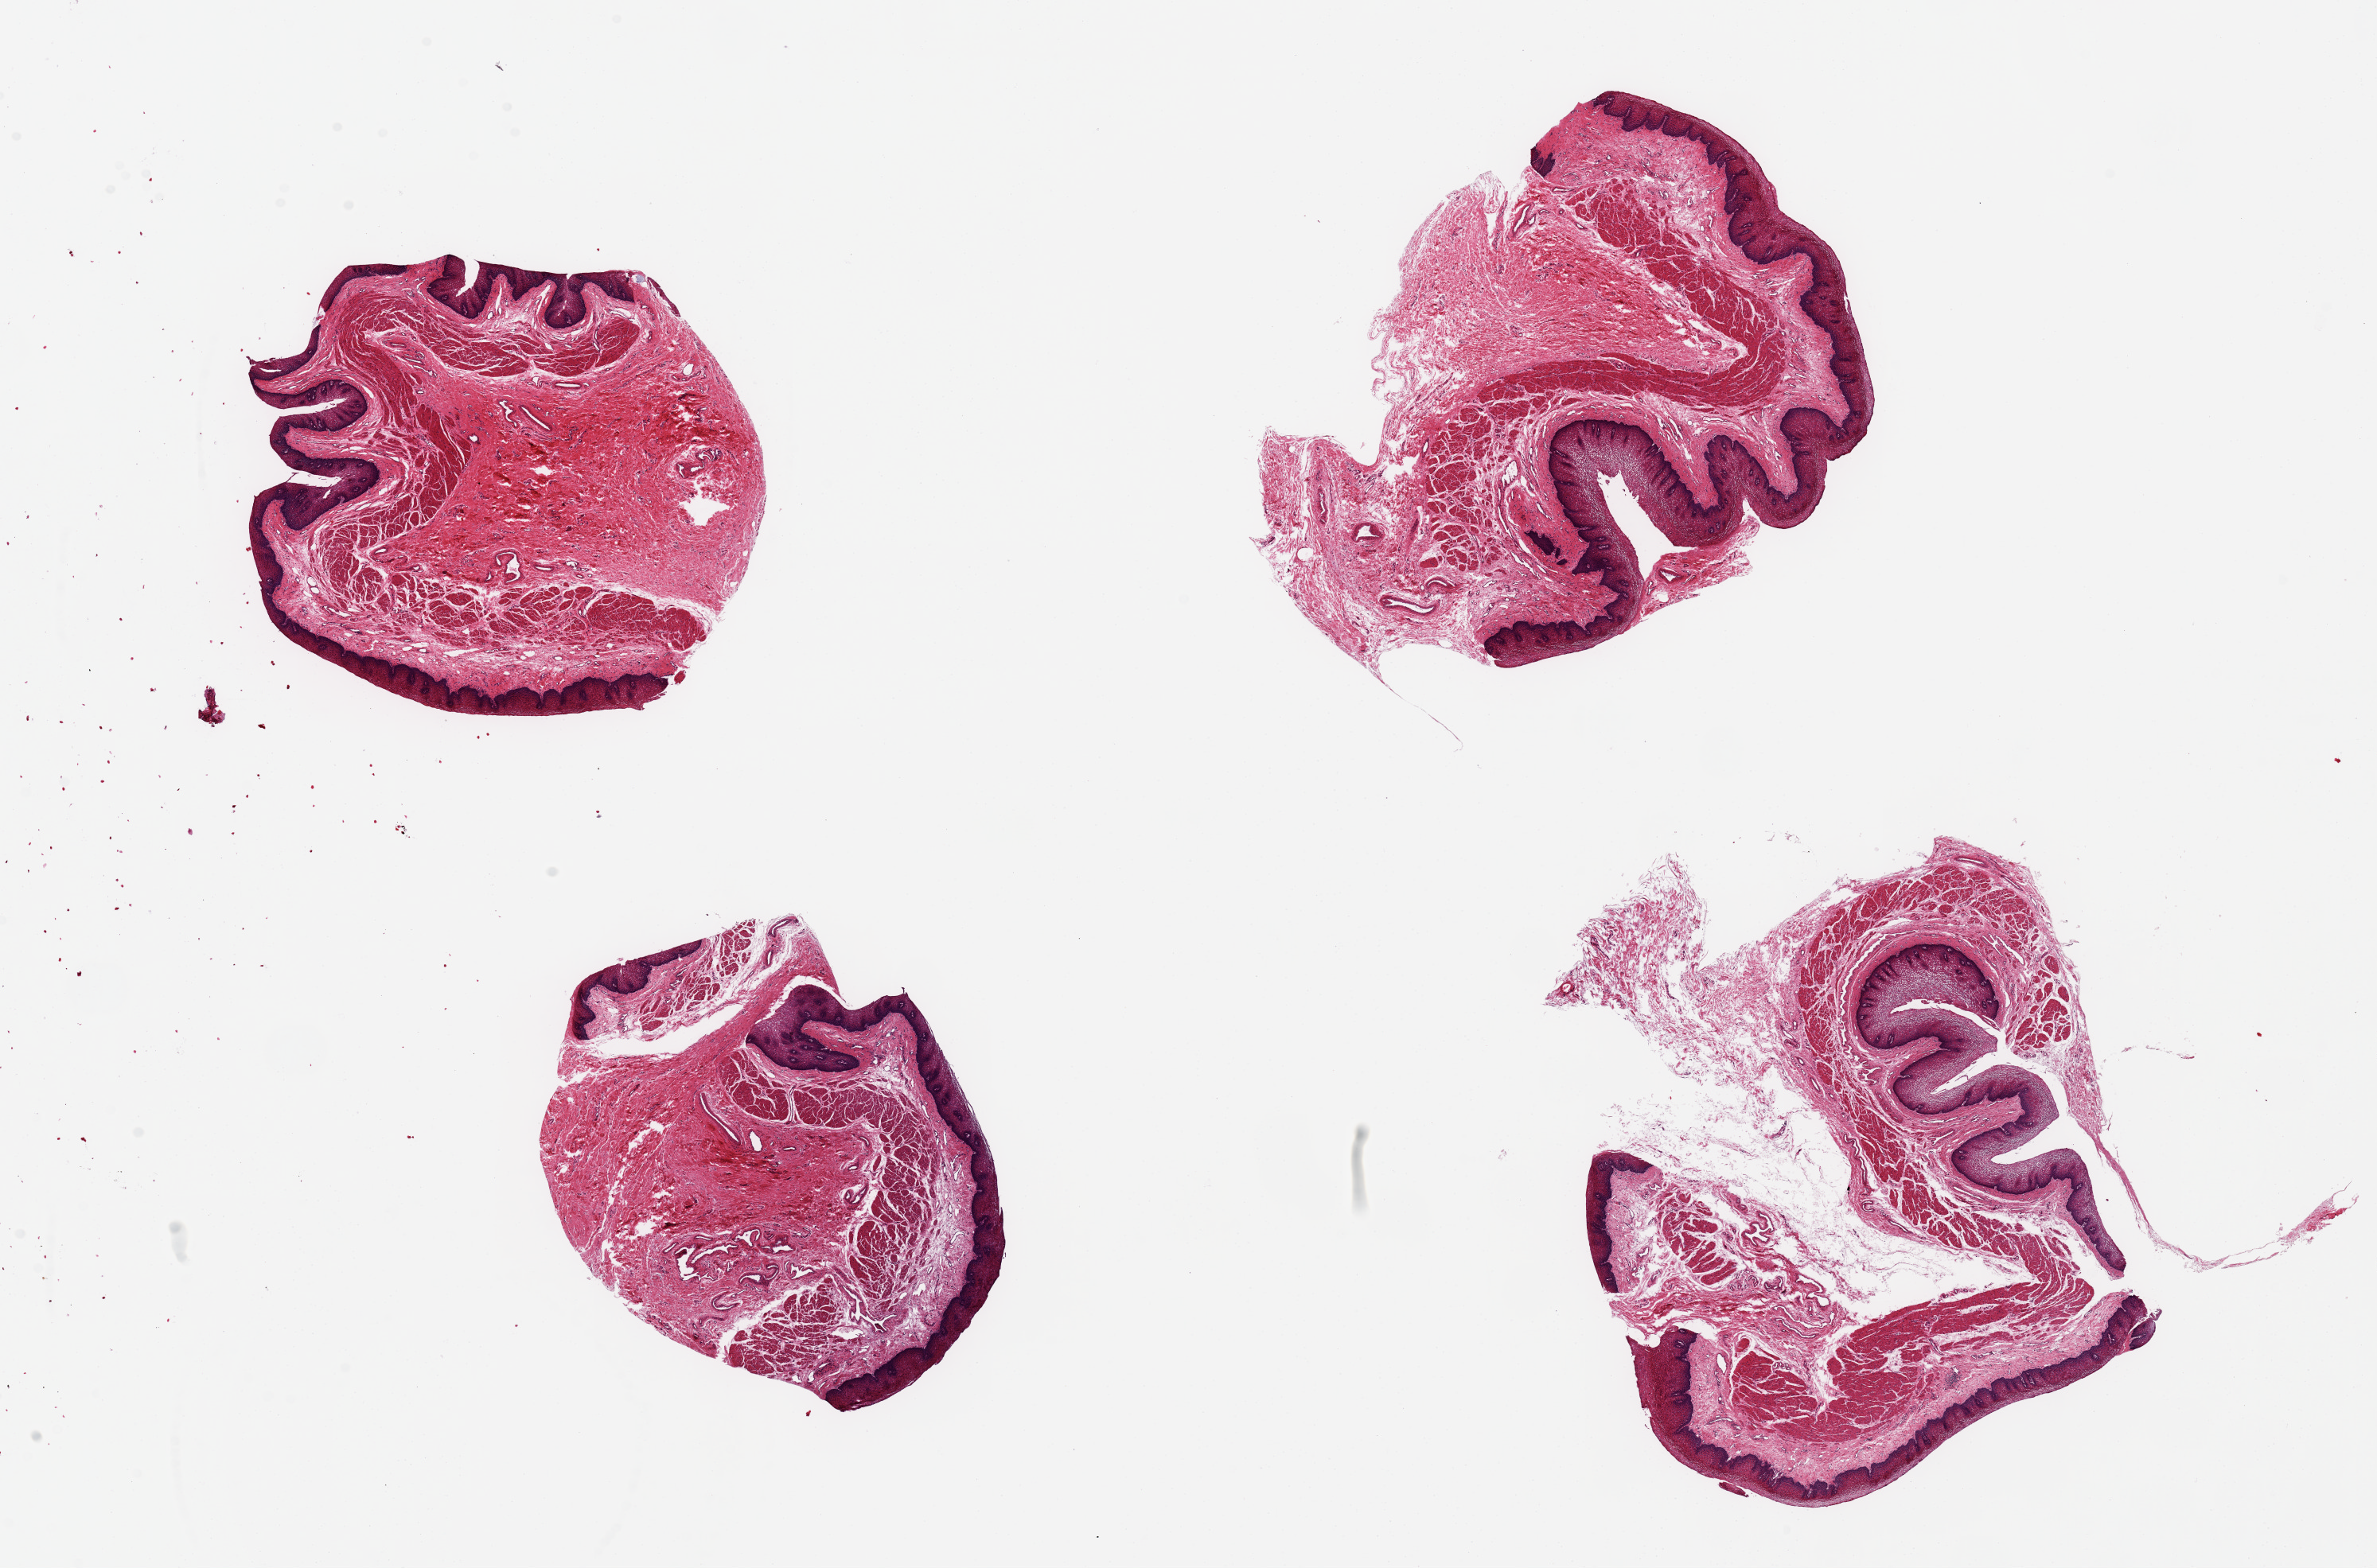
Haematoxylin and eosin whole-slide image, low-resolution overview of the scanned area, about 23.6 x 15.6 mm (from a 20x scan). PAXgene-fixed, paraffin-embedded tissue. Target tissue: esophageal mucous membrane. Donor tissue sample. Donor: female.
Reviewer comment on this tissue sample: 4 pieces, ~6x4 mm; some epithelium with excess glycogen.